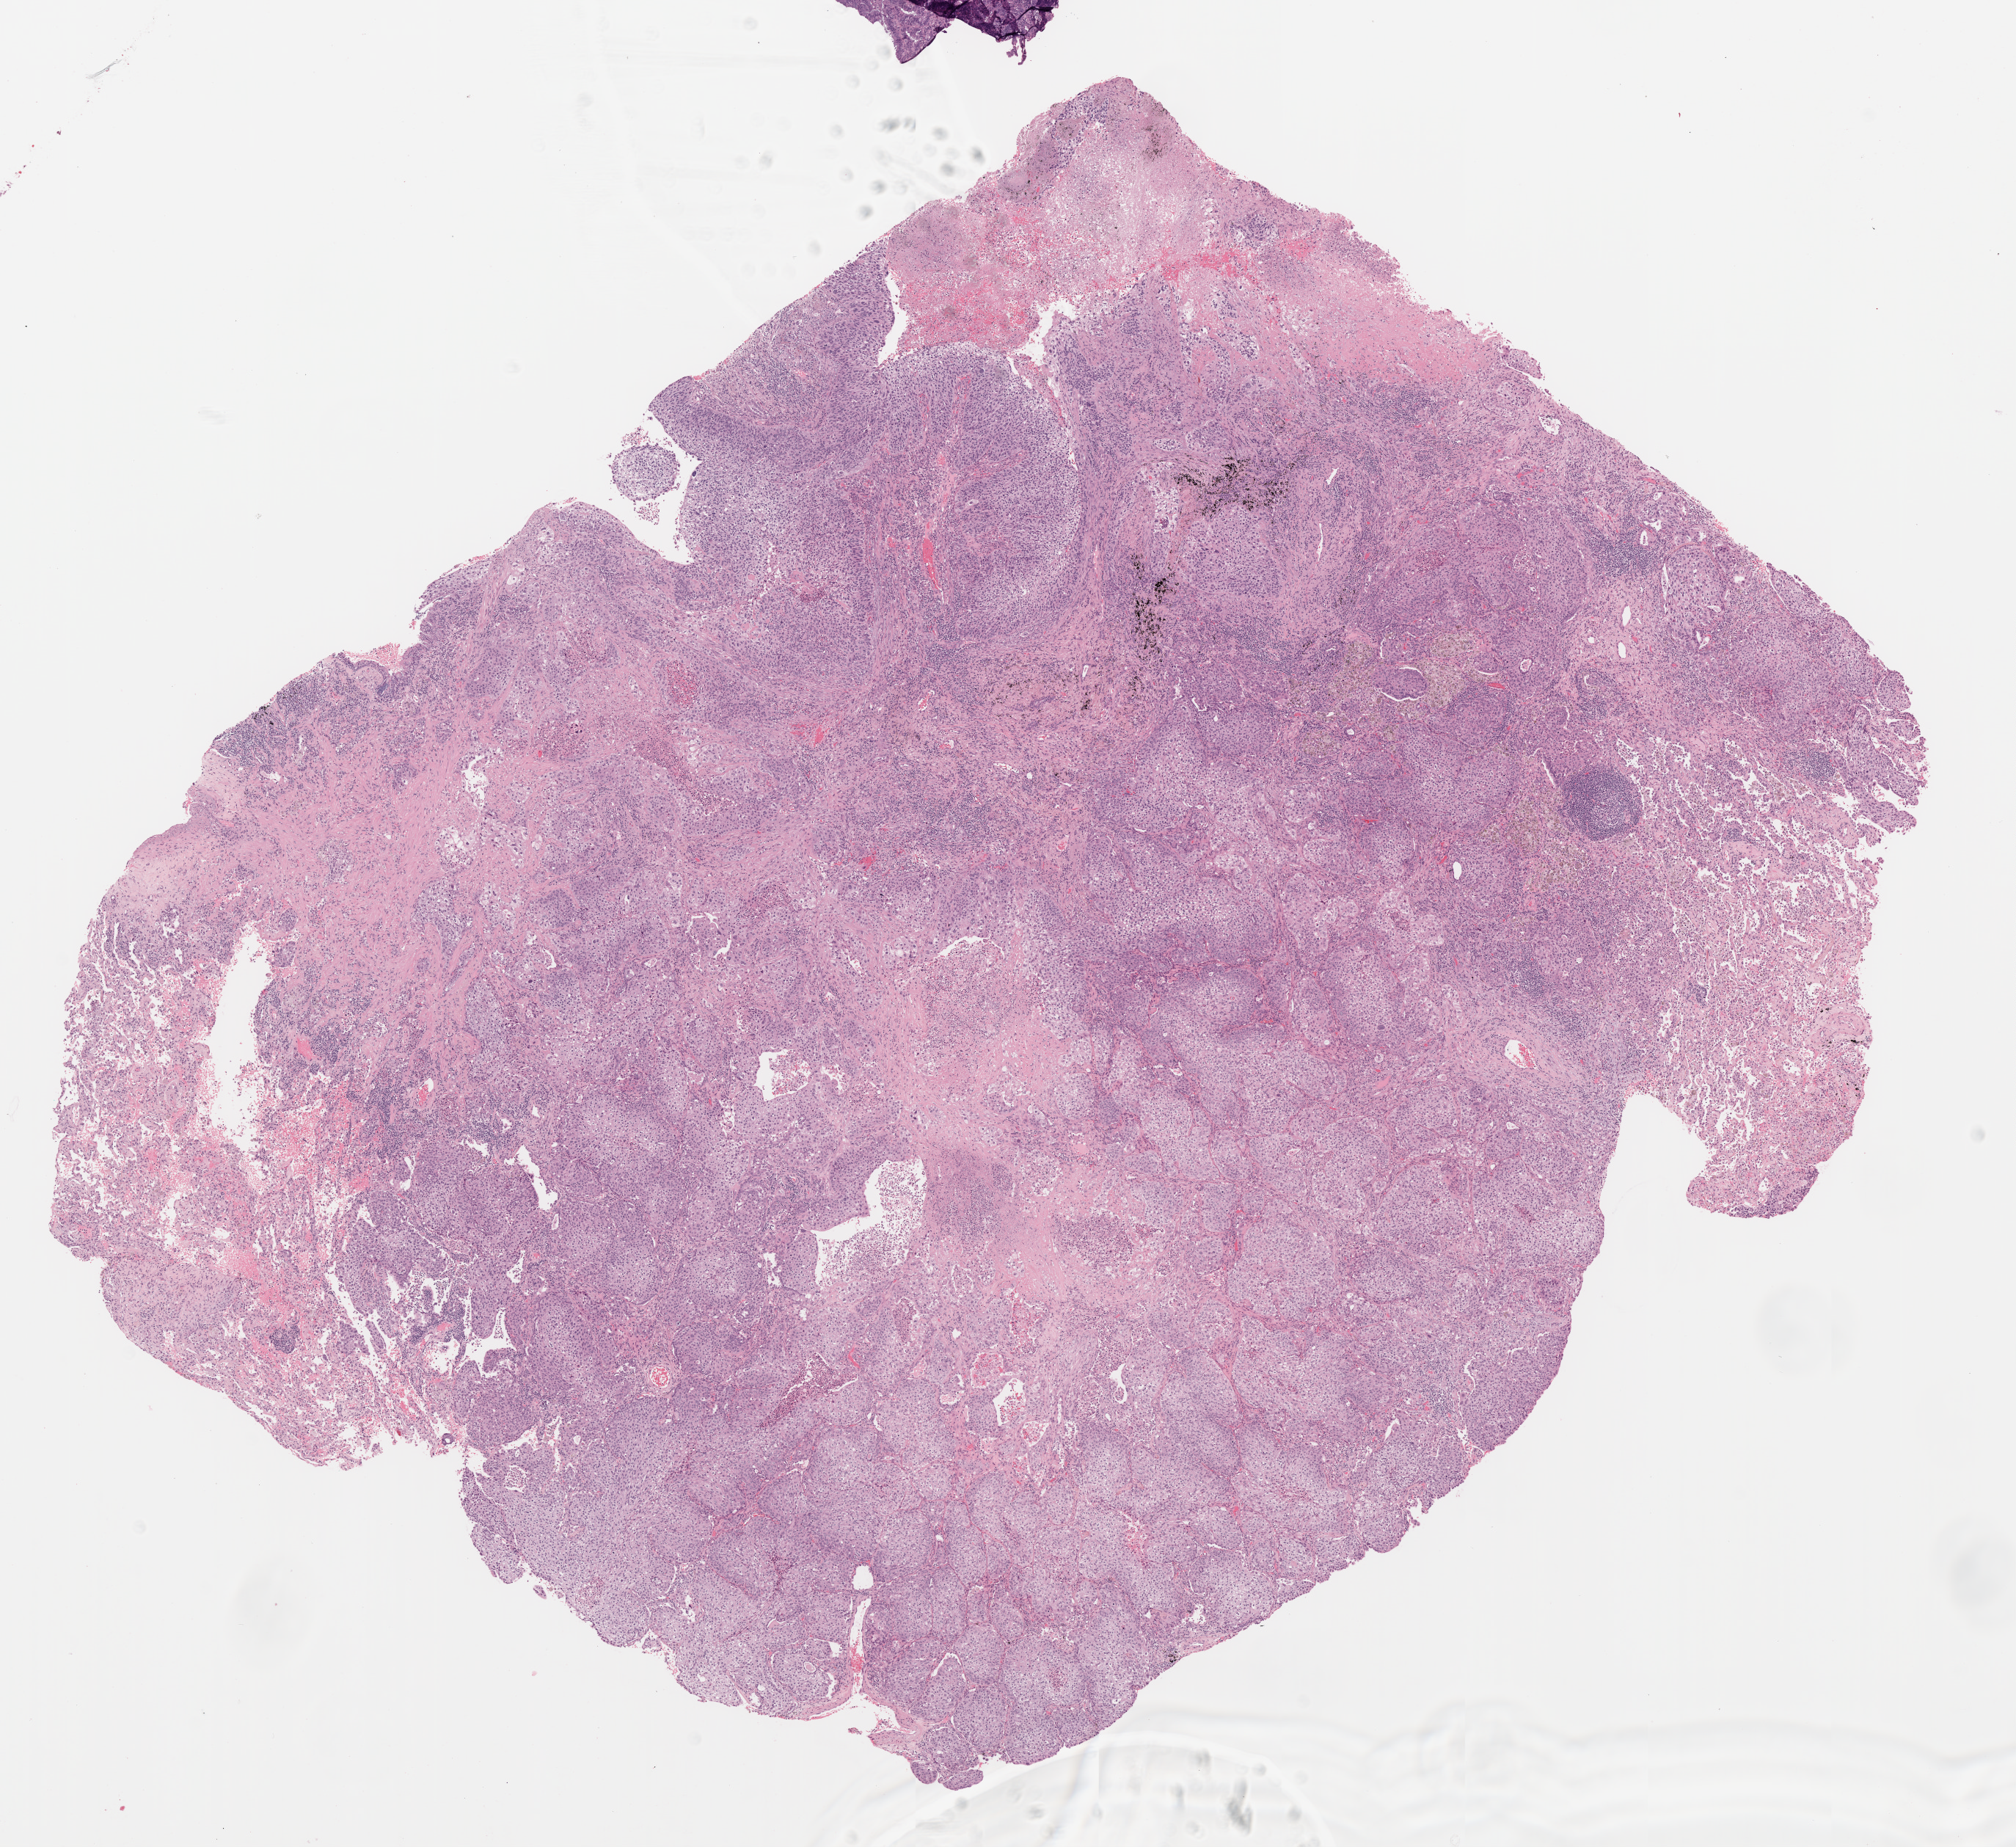
Whole-slide histology image, H&E — whole scanned area (about 11.0 x 10.1 mm, acquisition: 20x scan) shown as a low-resolution overview, FFPE section, sample: primary tumour, lung. Patient sex: male.
Diagnosis: Squamous cell carcinoma, NOS. AJCC pathologic stage: IA (6th edition).